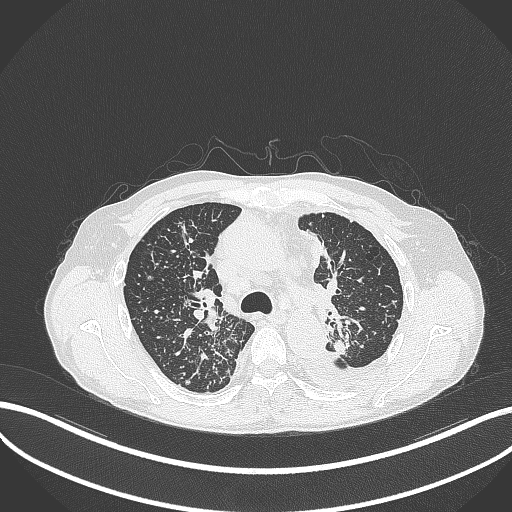
Chest CT, one axial slice; position 247 of 325 along the scan axis; reconstruction kernel B70f; 120 kVp; lung window (W 1500 / L -600 HU); 1 mm slice thickness; 512 × 512 image matrix, field of view 400 × 400 mm. Patient: male, 58 years. From the clinical record (not read from this slice): clinical TNM (as recorded): T1c N3 M1.
Outlined on this slice (bounding box drawn by a radiologist):
- lung tumour (recorded histology: adenocarcinoma): bounding box <330,339,351,360> (left, top, right, bottom; pixels)